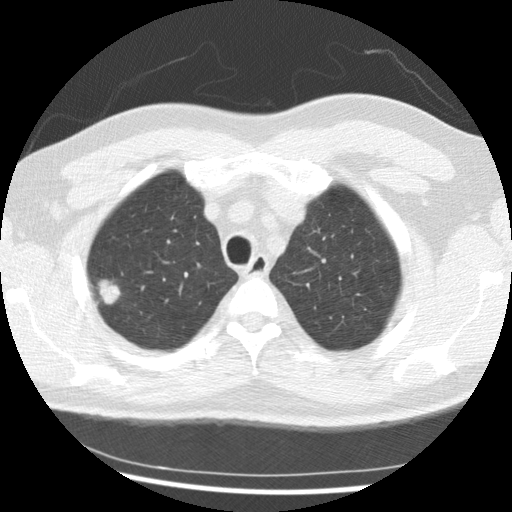
Chest CT (low-dose screening protocol), one axial image; first (baseline) screen; lung window (W 1500 / L -600 HU); slice 50 of 265 in the series; 512 × 512 image matrix, field of view 340 × 340 mm. Male, age 56 years at enrolment. Current smoker at enrolment.
Expert reader's lesion annotation, bounding box [x1, y1, x2, y2] px = [84, 273, 132, 315]. Screening reader's record for this exam (one nodule recorded; not confirmed to be the boxed lesion): non-calcified nodule or mass ≥4 mm, right upper lobe, 19 × 15 mm, spiculated (stellate) margins, soft tissue attenuation. Official screen result: positive, change unspecified: nodule(s) >= 4 mm or enlarging nodule(s), mass(es), or other non-specific abnormalities suspicious for lung cancer. Lung cancer was diagnosed 291 days after this screen: non-small cell carcinoma, right upper lobe, poorly differentiated (G3), stage IIIB (AJCC 6th edition), 20 mm at pathology.